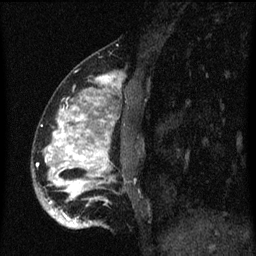
Breast MRI (dynamic contrast-enhanced), one sagittal slice; position 19 of 60 along the scan axis; dynamic contrast-enhanced series, image 2 of 3 at this slice position (ordered by acquisition); 1.5 T; TE 4.2 ms, TR 8.4 ms; 256 × 256 image matrix, field of view 180 × 180 mm. Female patient, age 34 years. From the clinical record (not read from this slice): setting: breast cancer imaged before/during neoadjuvant chemotherapy; receptor status: HR-positive, HER2-negative.
Annotated regions visible in this slice (semi-automatically segmented with operator editing):
- analysis volume of interest (the breast-tissue region the enhancement analysis was run in; not a lesion): box from (x=32, y=60) to (x=141, y=229) px
- tumour enhancement mask (voxels above the 70 % enhancement threshold inside the analysis volume of interest): (x=46, y=76)–(x=119, y=227)